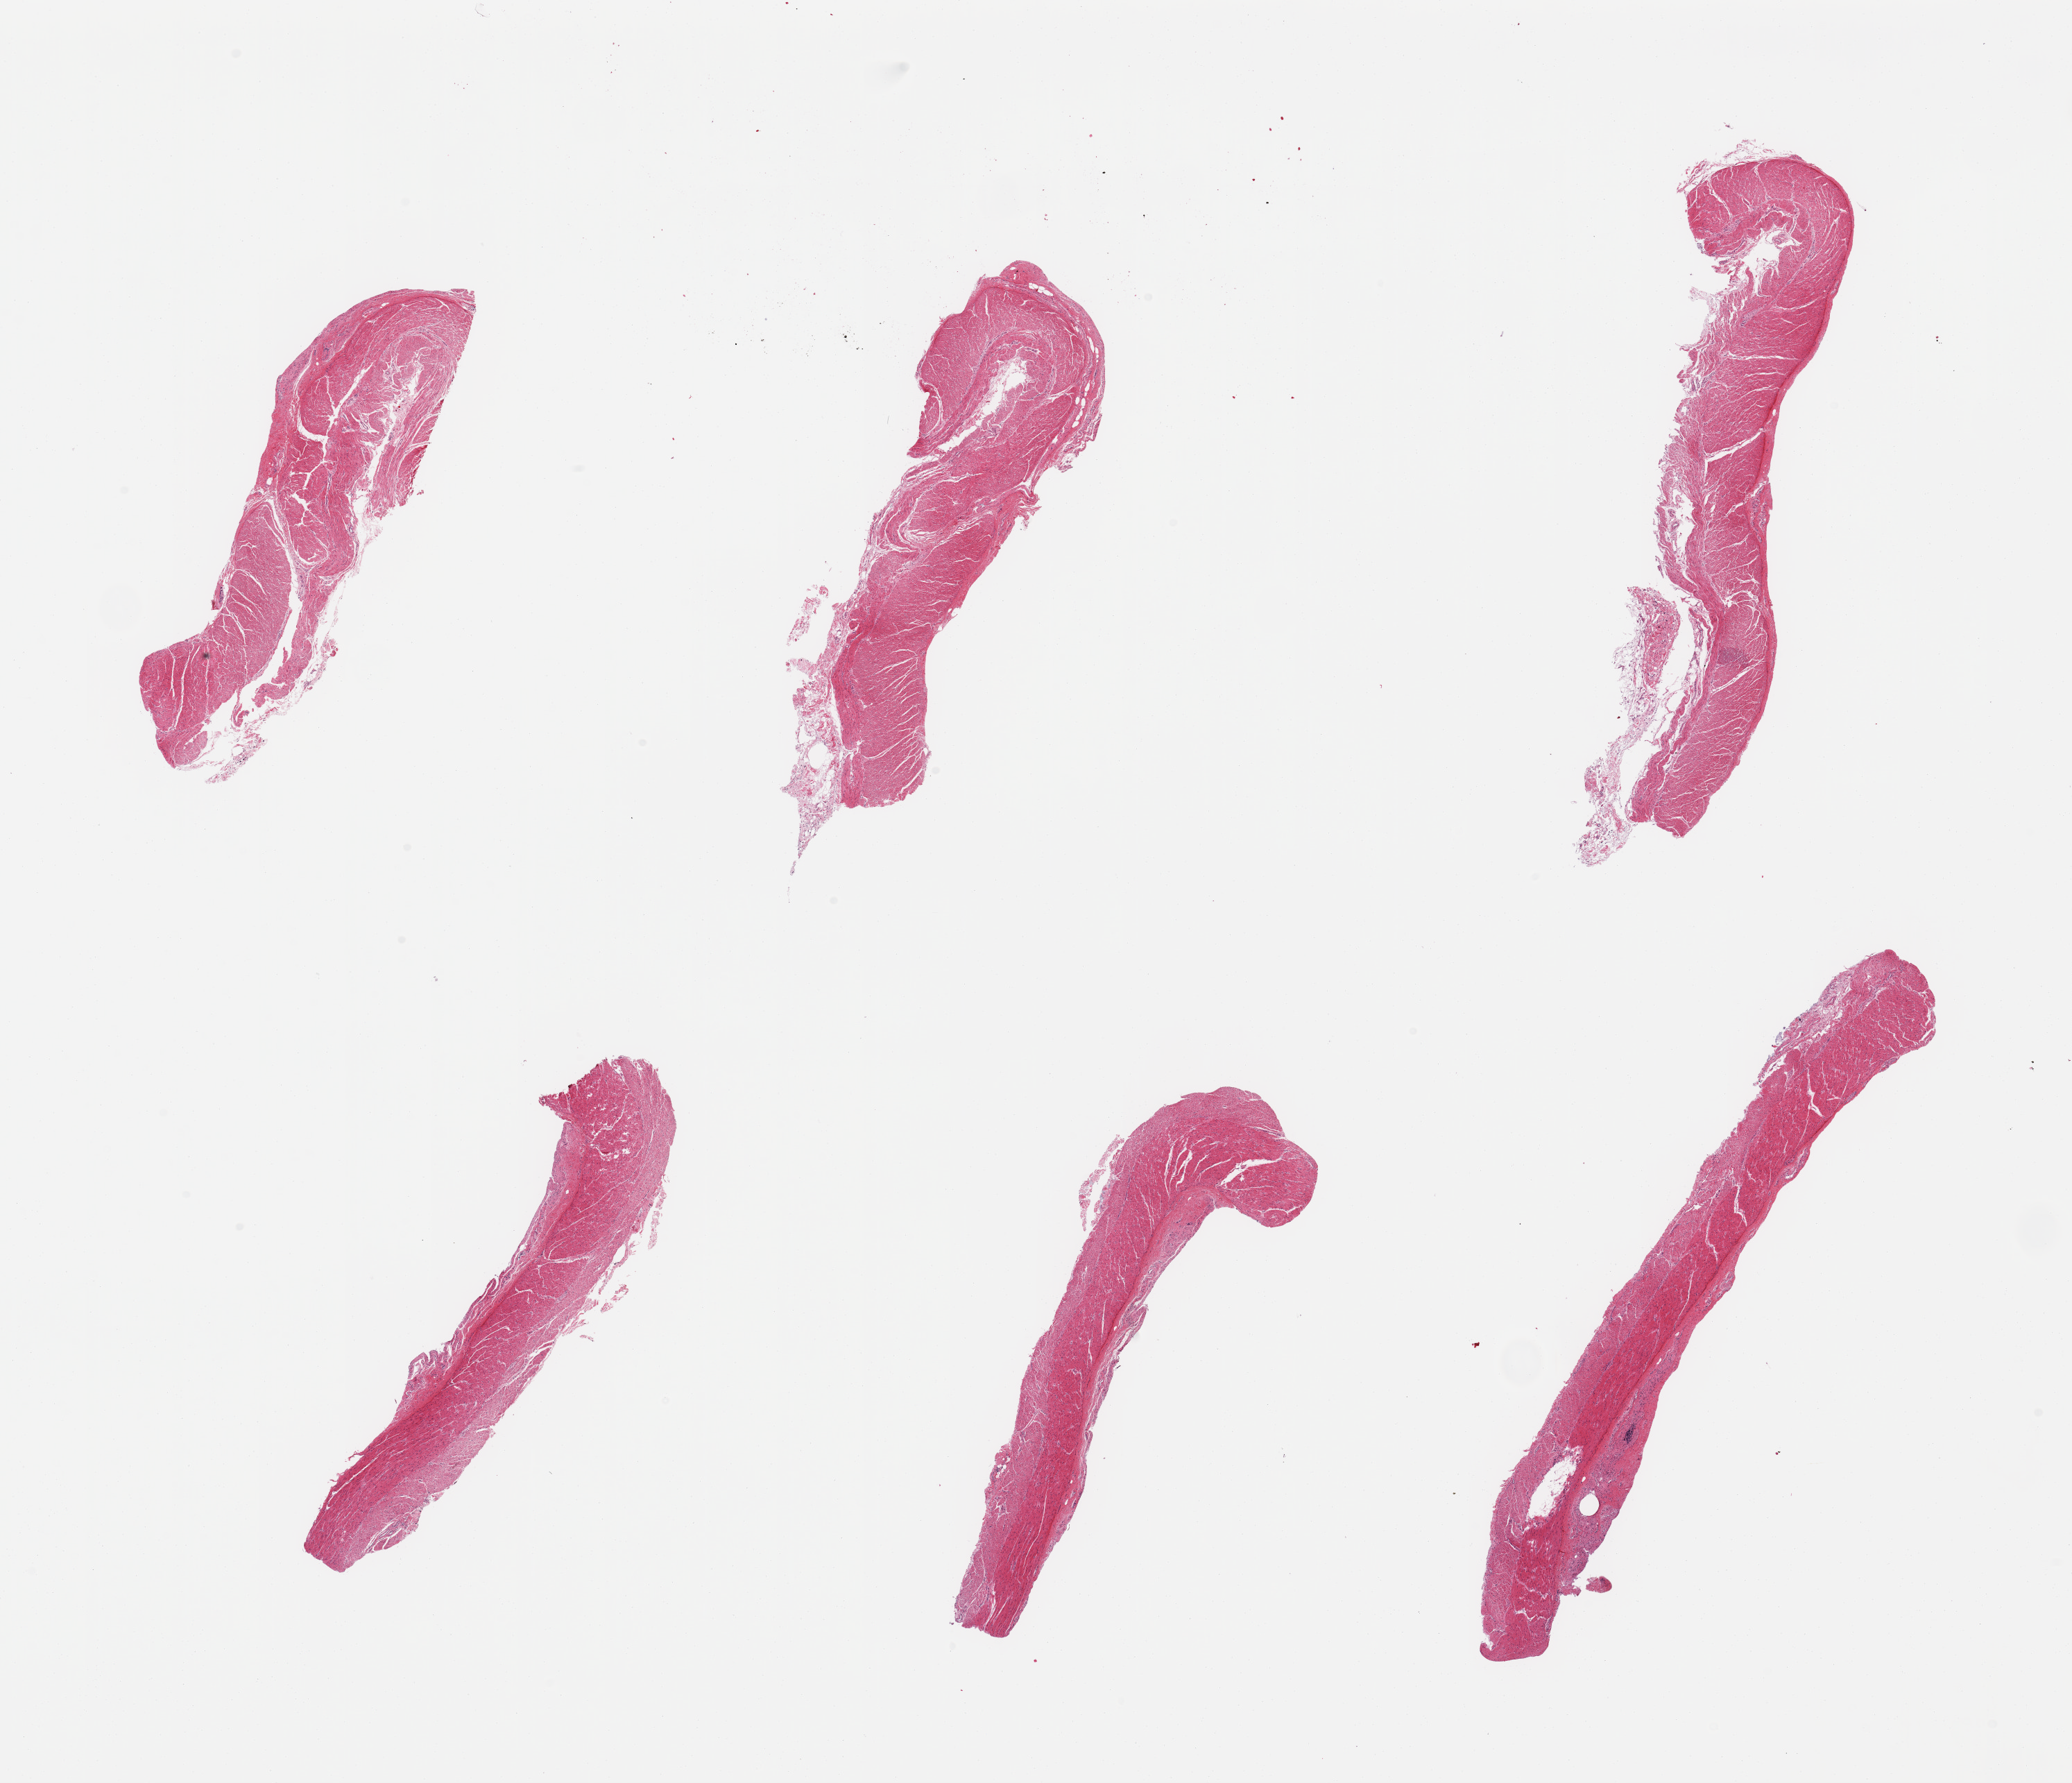
Haematoxylin and eosin whole-slide image, brightfield — shown as a low-resolution overview of the whole scanned area (about 23.6 x 20.3 mm, acquisition: 20x scan), PAXgene-fixed paraffin-embedded (PFPE) section, target tissue: sigmoid colon, tissue donor sample. Donor: female.
Review note (as recorded): 6 pieces; target muscularis.